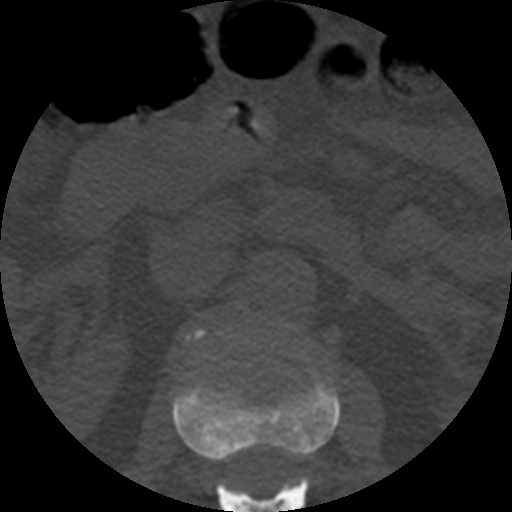
CT including the spine, one axial slice; reconstruction kernel STANDARD; 120 kVp; bone window (W 1800 / L 400 HU); 1.25 mm slice thickness; 512 × 512 image matrix, field of view 160 × 160 mm. Patient age 57 years. Case-level facts recorded for this patient, not image findings: primary cancer: prostate.
Structures marked on this image (semi-automatic segmentation, software-assisted and operator-edited):
- L1 vertebra: box from (x=173, y=381) to (x=340, y=512) px
- L2 vertebra: (x=194, y=331)–(x=203, y=337)